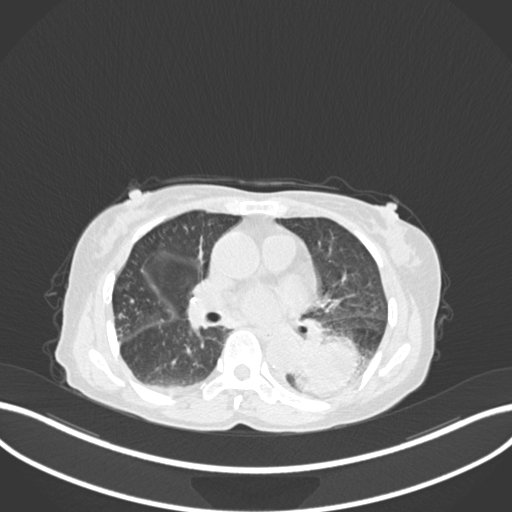
Chest CT, one axial slice; position 85 of 233 along the scan axis; 120 kVp; lung window (W 1500 / L -600 HU); 512 × 512 image matrix, field of view 400 × 400 mm. Female patient, age 78 years. From the clinical record (not read from this slice): clinical TNM (as recorded): T3 N0 M1.
Outlined on this slice (bounding box drawn by a radiologist):
- lung tumour (recorded histology: squamous cell carcinoma): bounding box [x1, y1, x2, y2] px = [292, 333, 365, 398]